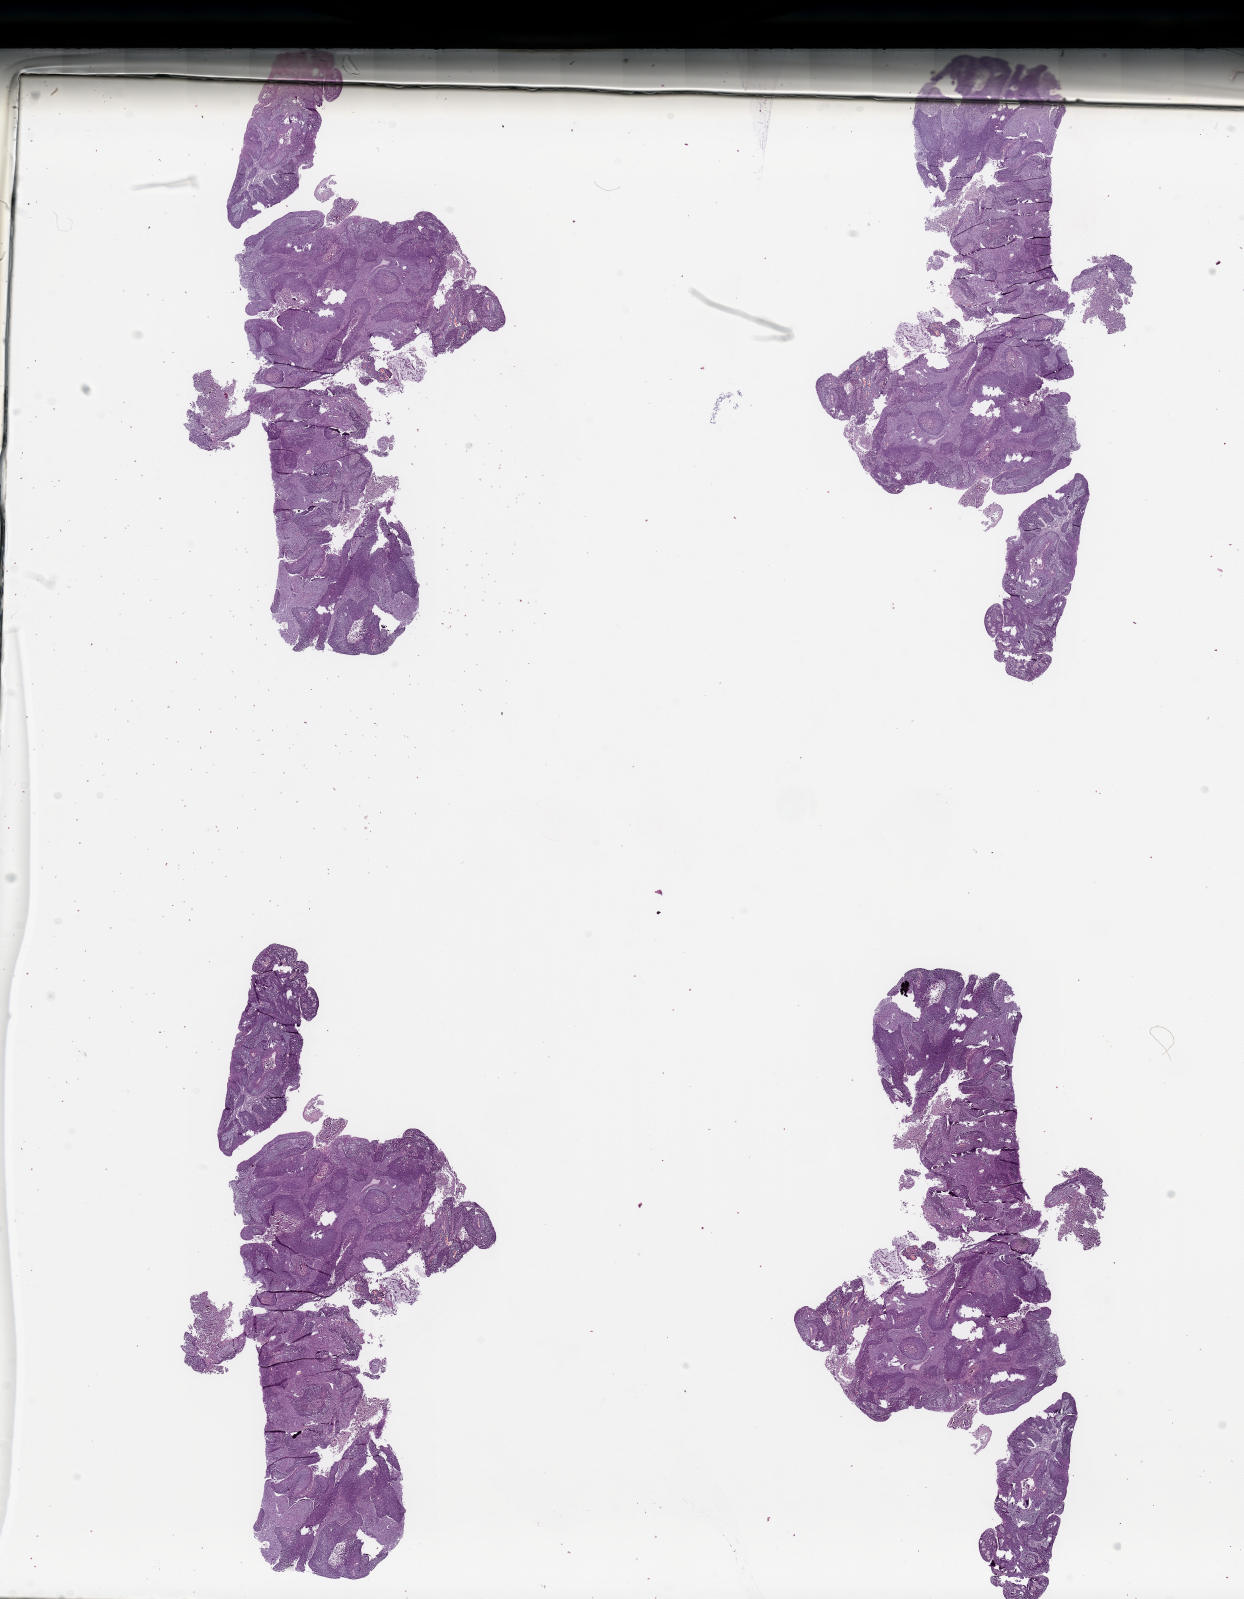
Whole-slide histology image, Hematoxylin and eosin (H&E) stained, low-resolution overview of the scanned area, about 19.7 x 25.3 mm, head and neck, tissue type not recorded. Patient: male, age 53 years.
• patient diagnosis: Squamous cell carcinoma, NOS (oropharynx, NOS)